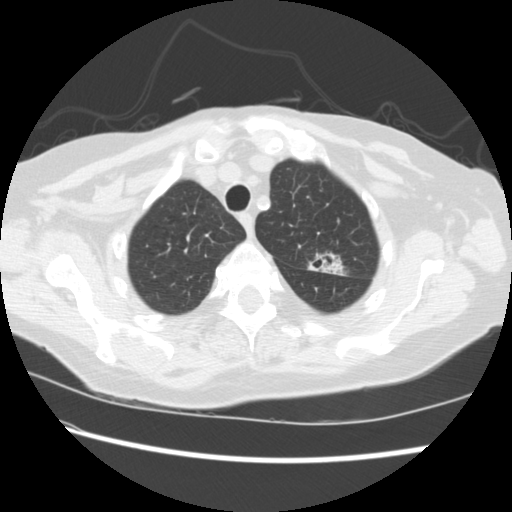
Low-dose screening chest CT, one axial slice. Slice 182 of 224 in the series (ordered by position). Reconstruction kernel STANDARD. Lung window (W 1500 / L -600 HU). 2.5 mm slice thickness. 512 × 512 image matrix, field of view 340 × 340 mm.
Outlined on this slice (outlined manually by an expert reader):
- lesion 1 (tumor, upper lobe of left lung): bounding box <320,258,345,276> (left, top, right, bottom; pixels)